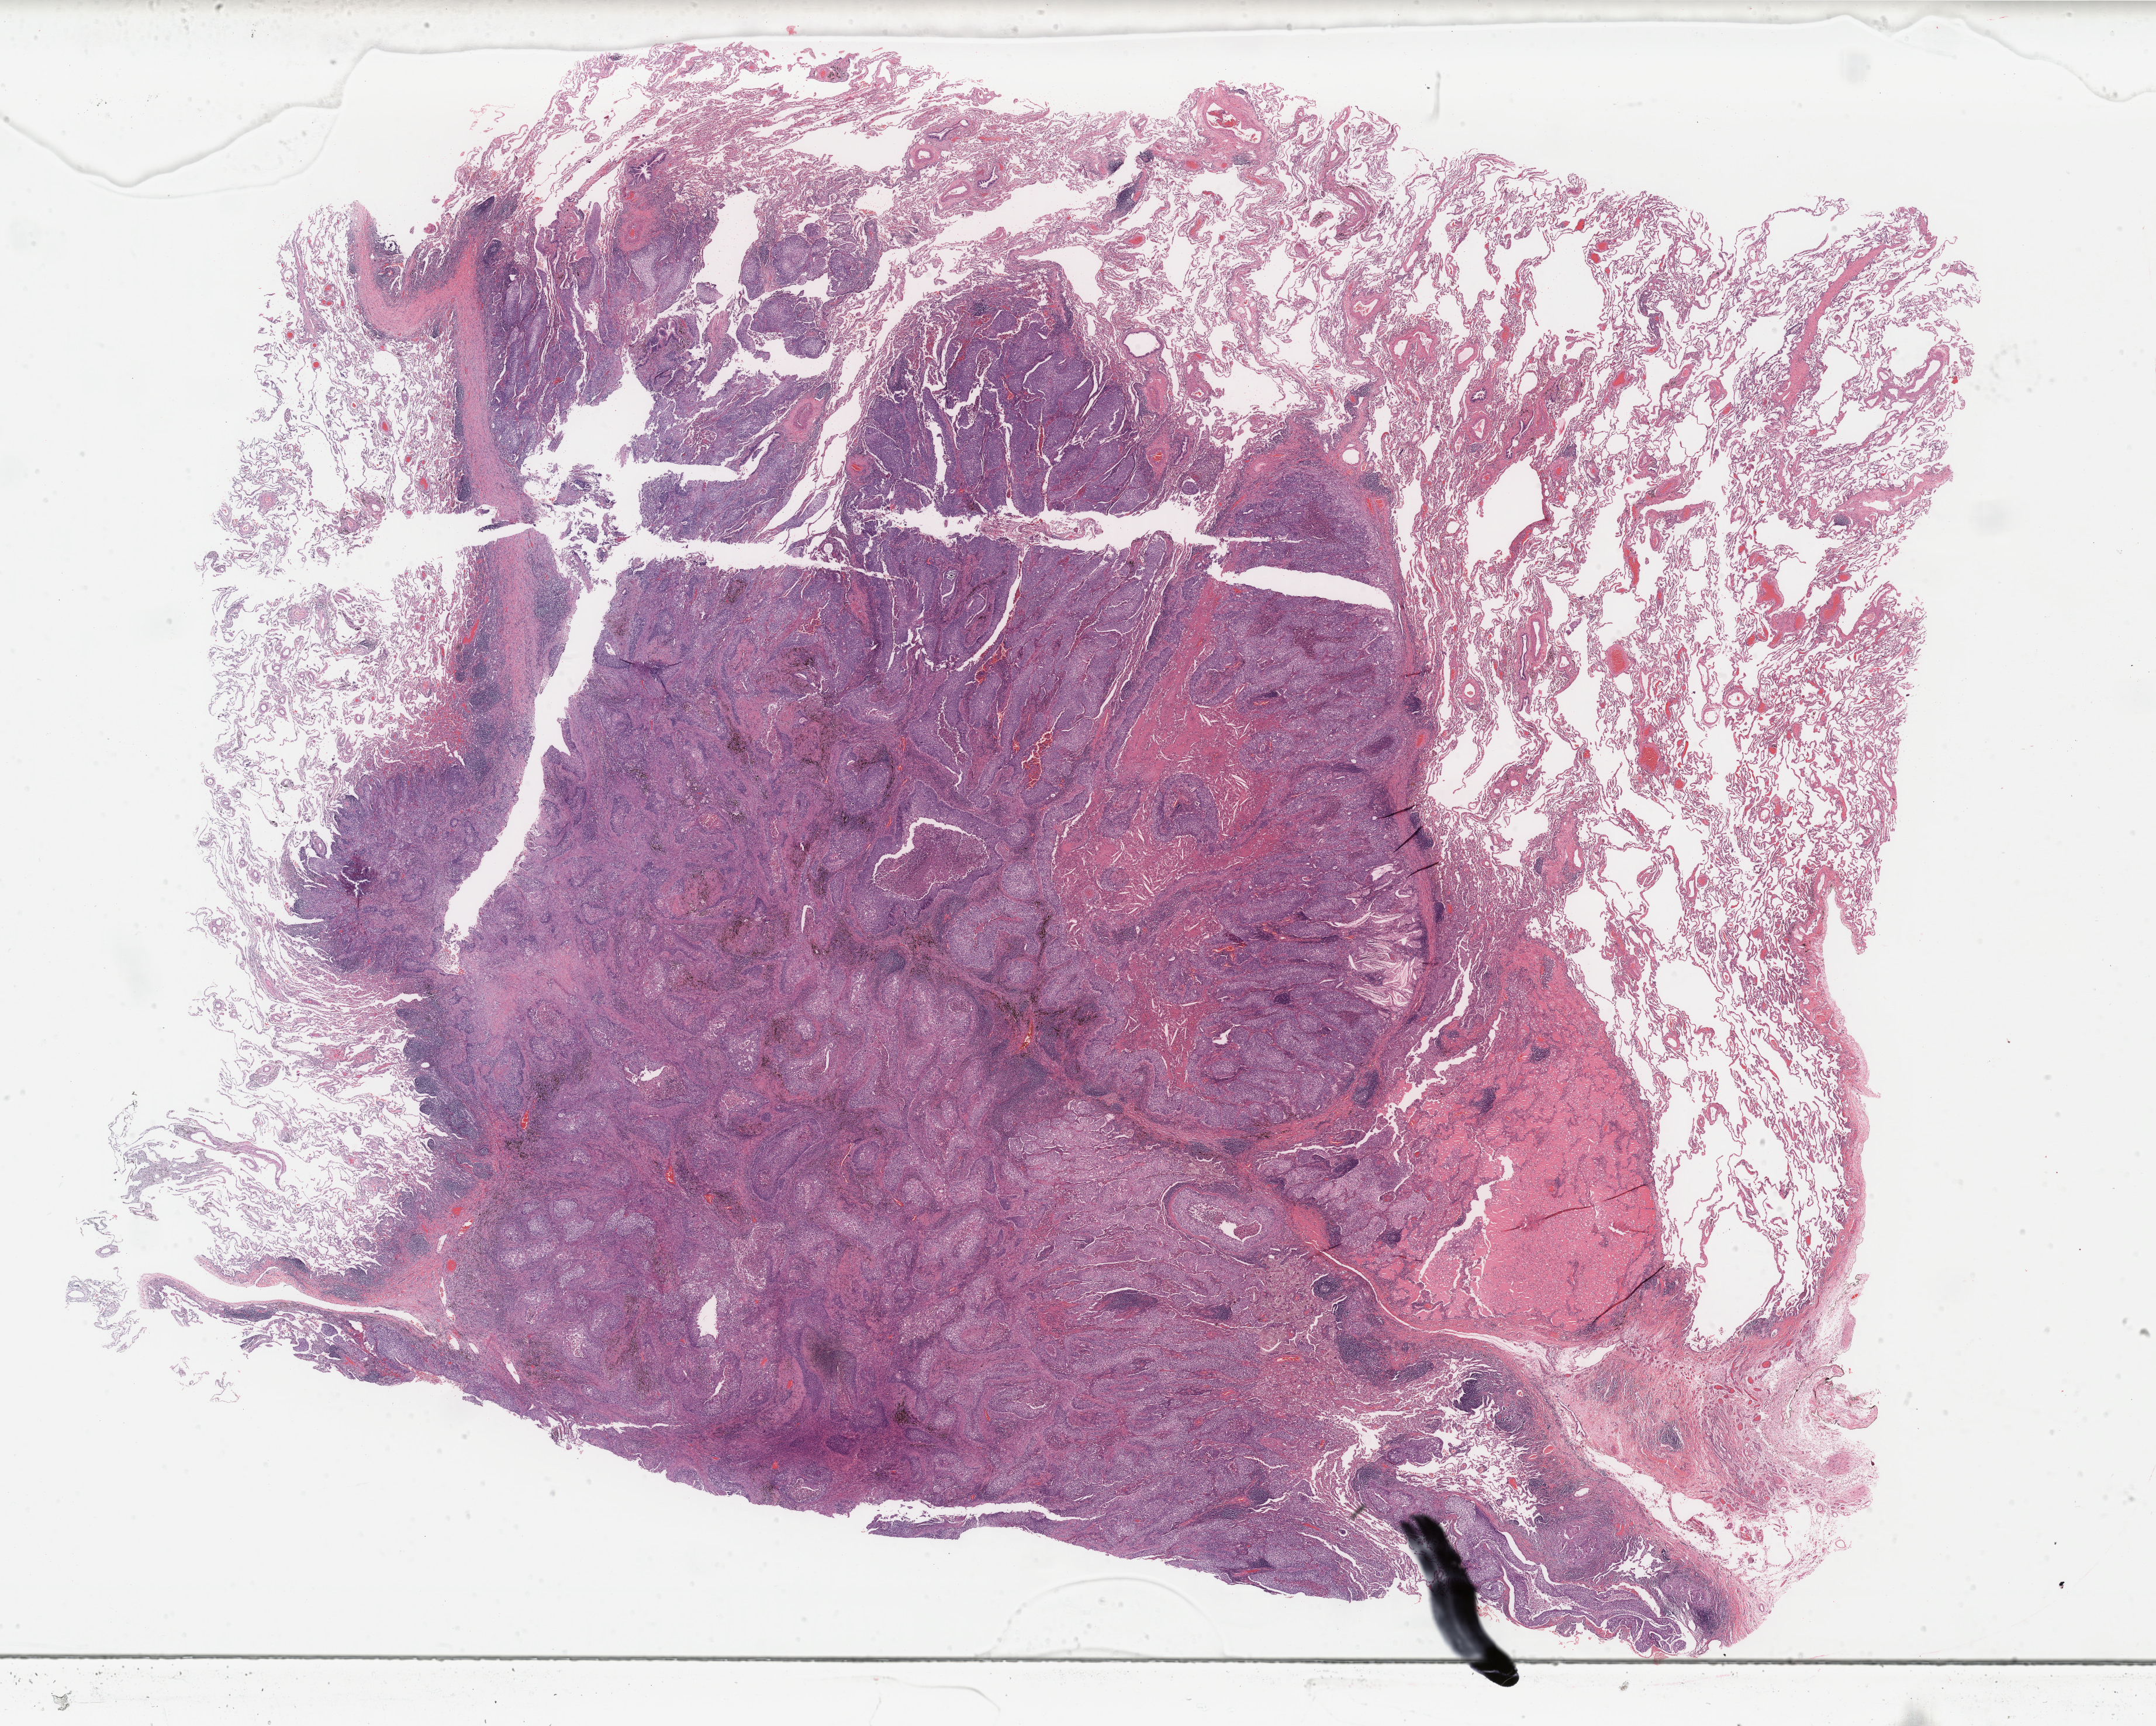
Whole-slide histology image, Hematoxylin and eosin (H&E) stained, low-resolution overview of the scanned area, about 29.3 x 23.4 mm; formalin-fixed paraffin-embedded (FFPE) diagnostic section; primary tumour sample from the lung. Male, age 66 years at initial diagnosis.
Histologic diagnosis: Squamous cell carcinoma, NOS (upper lobe, lung).